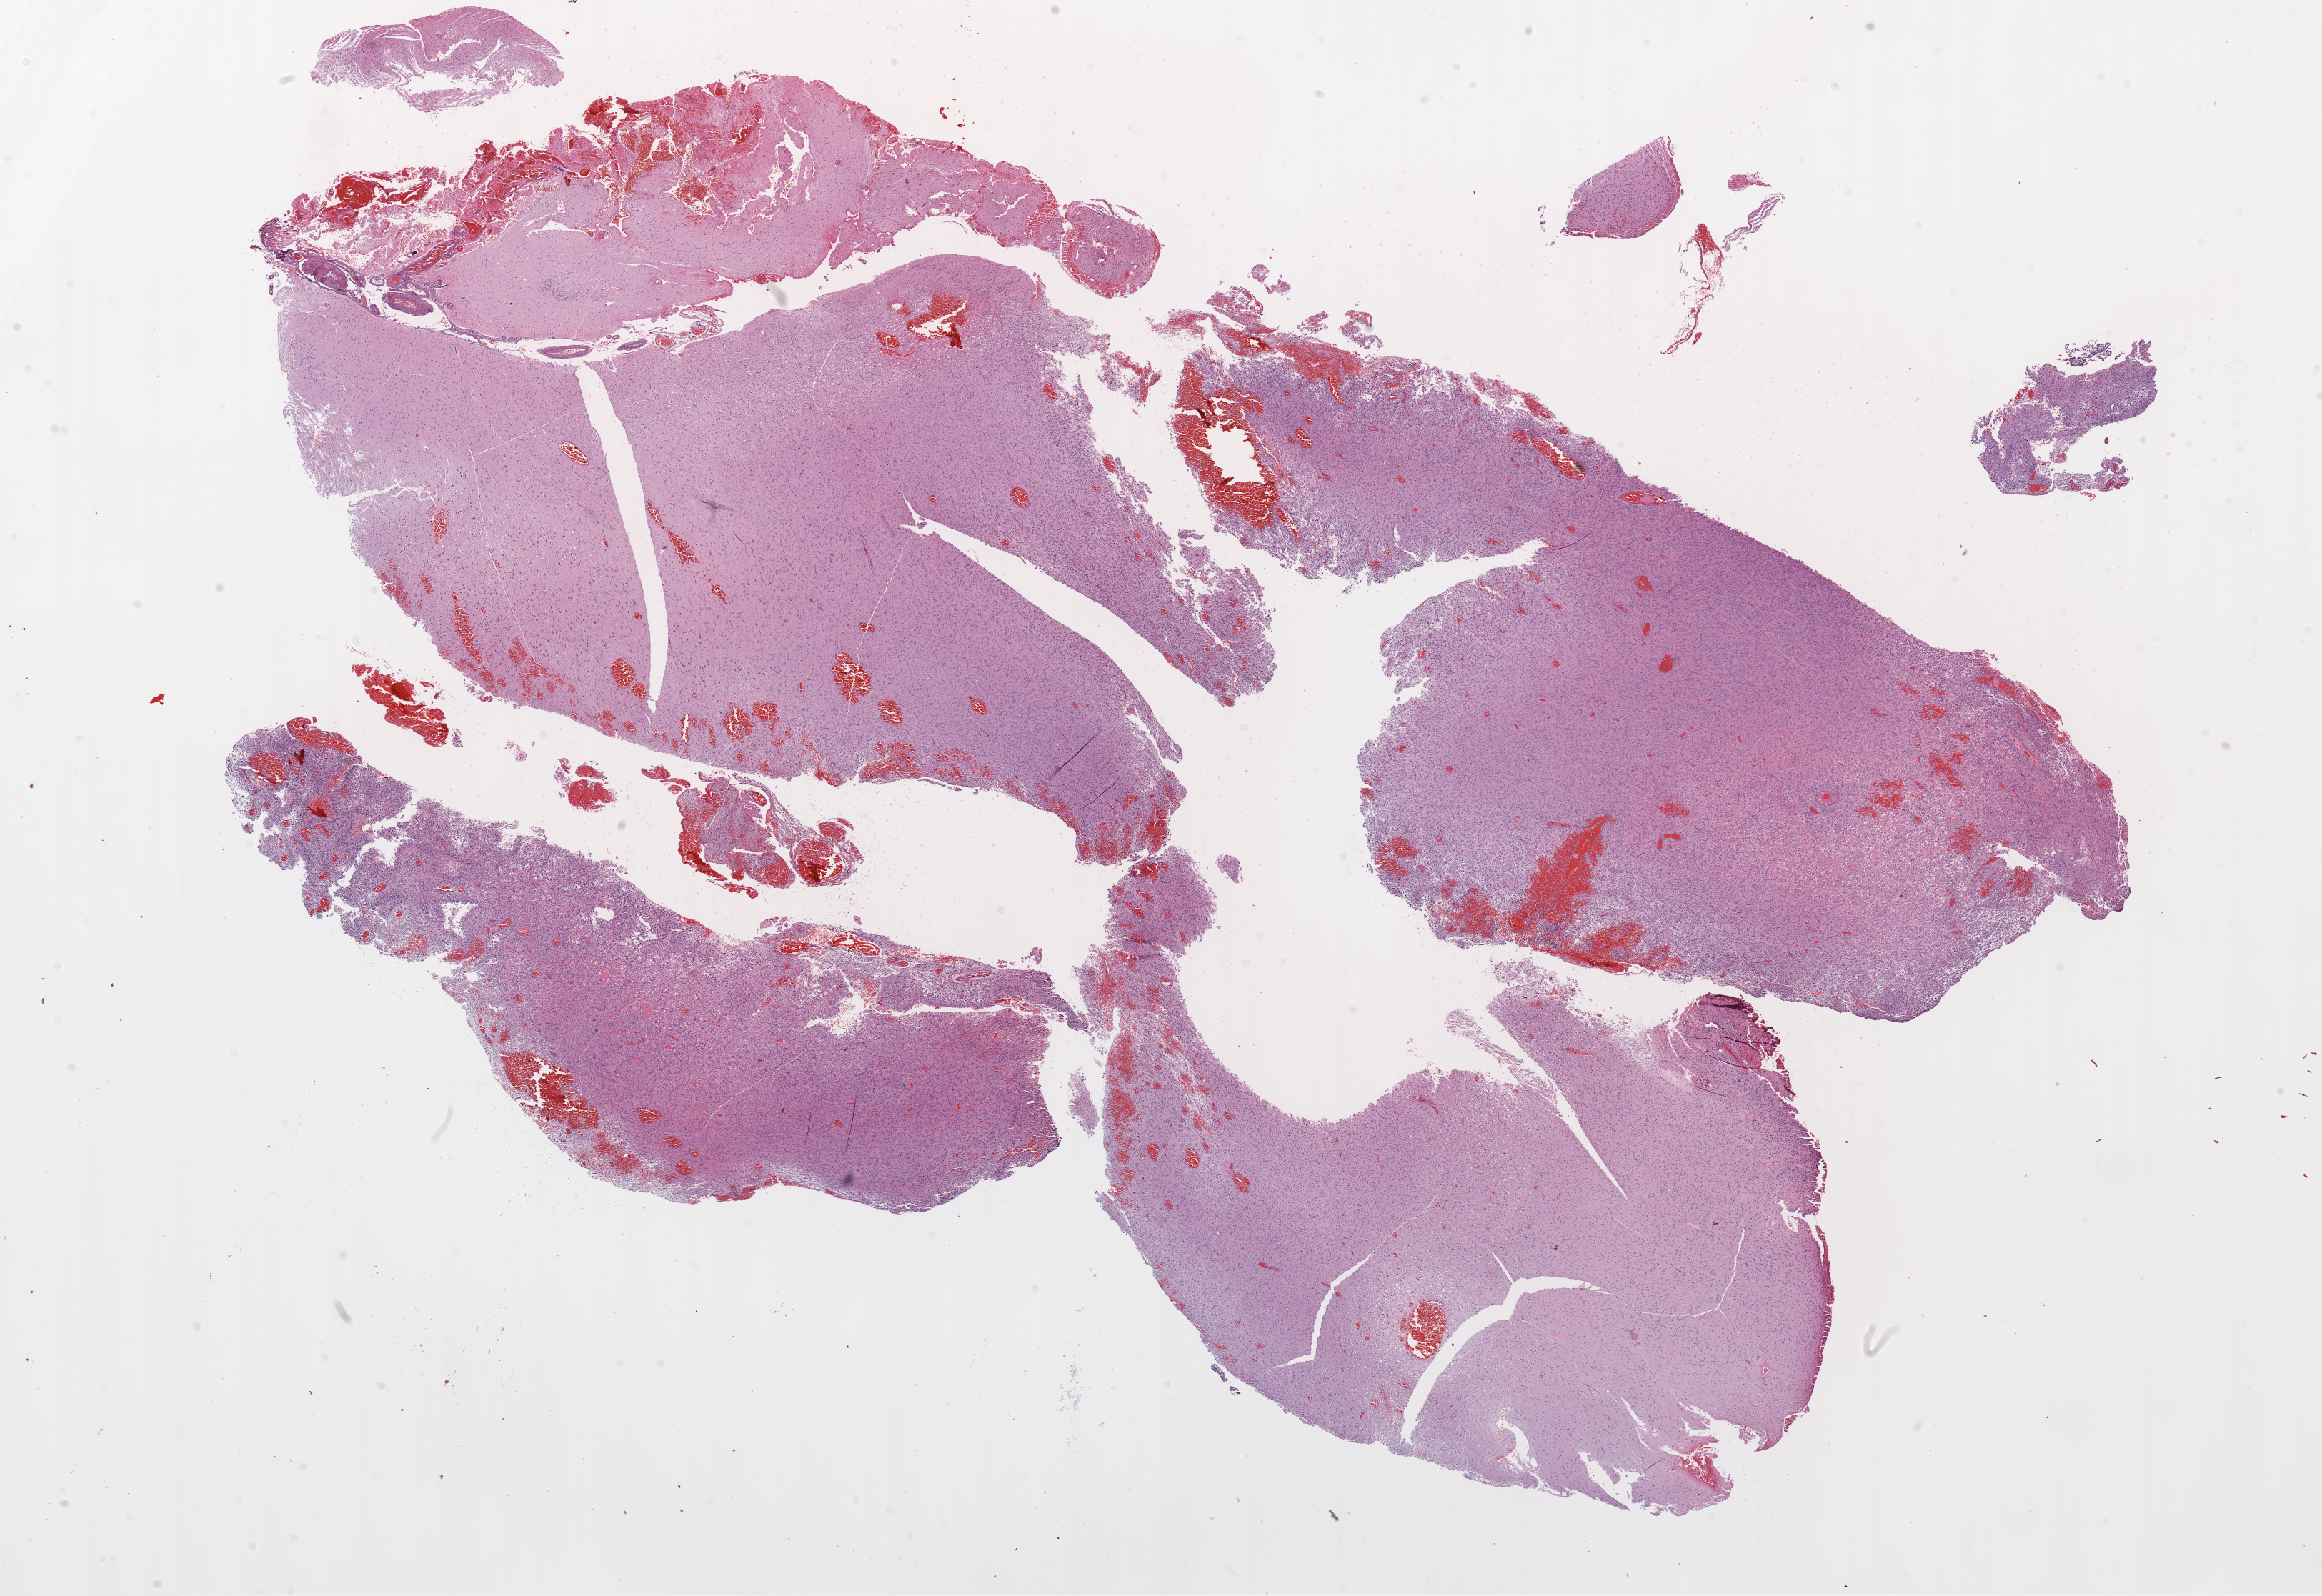
Whole-slide histology image, H&E-stained — a low-resolution overview of the entire scanned area, about 26.1 x 17.9 mm; formalin-fixed paraffin-embedded (FFPE) diagnostic section; brain, primary tumour sample. Male, age 60 years at initial diagnosis.
* diagnosis: Glioblastoma